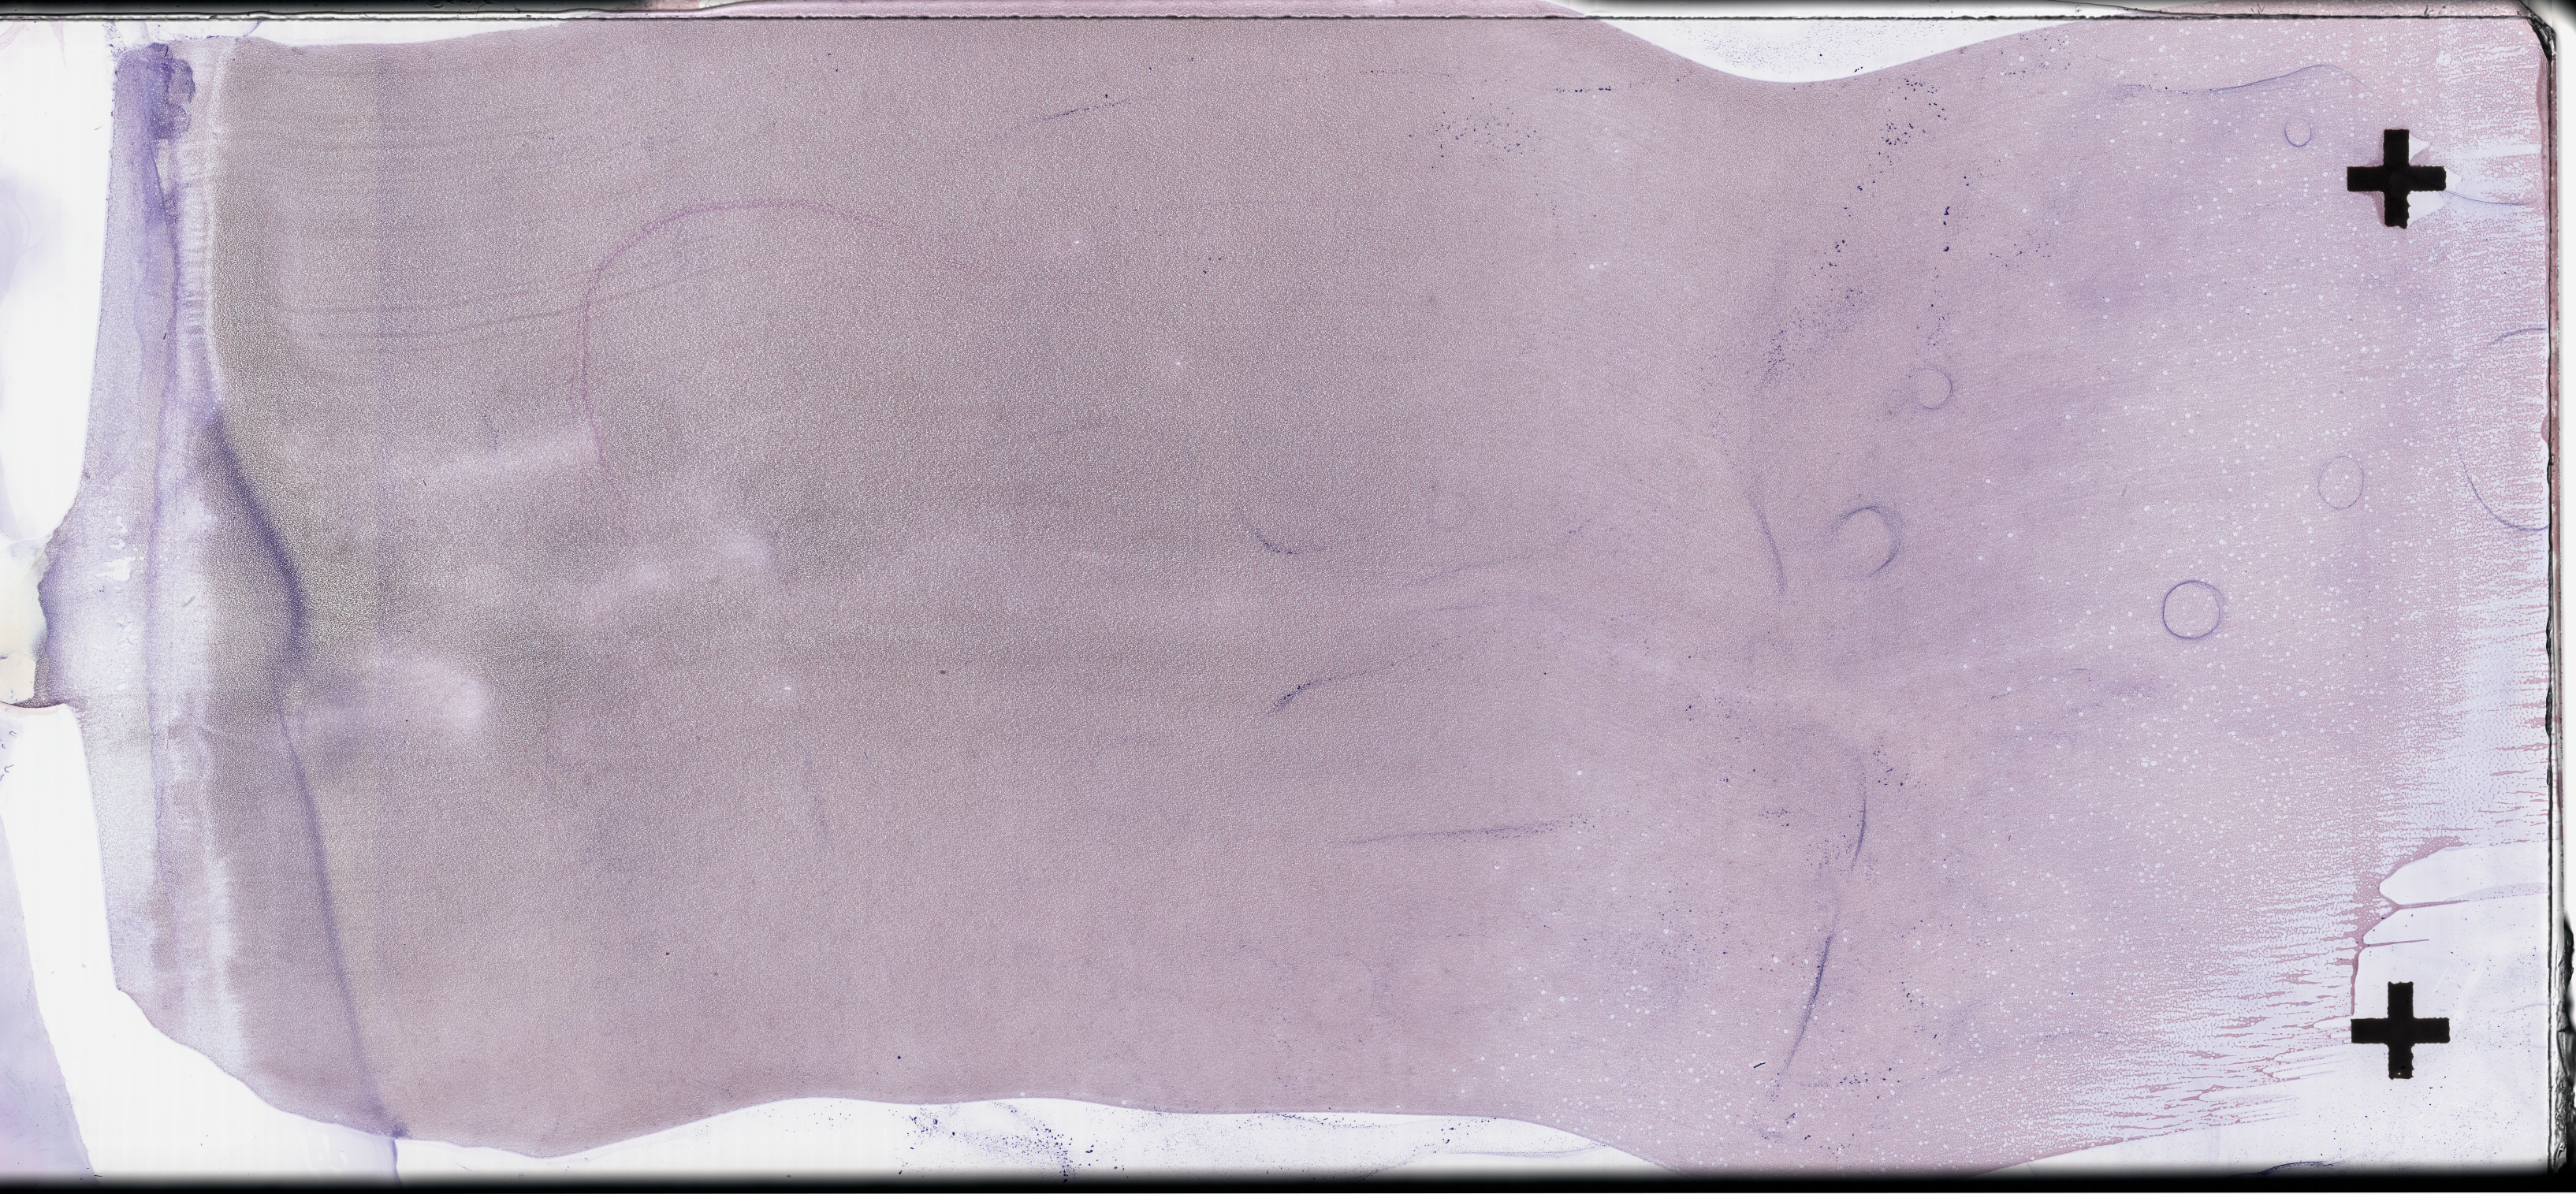
Whole-slide image of a whole blood smear, Wright–Giemsa stain — a low-resolution overview of the entire scanned area, about 52.8 x 24.5 mm, EDTA-anticoagulated smear, collected on treatment. Patient sex: male.
Patient diagnosis: Plasma Cell Myeloma.